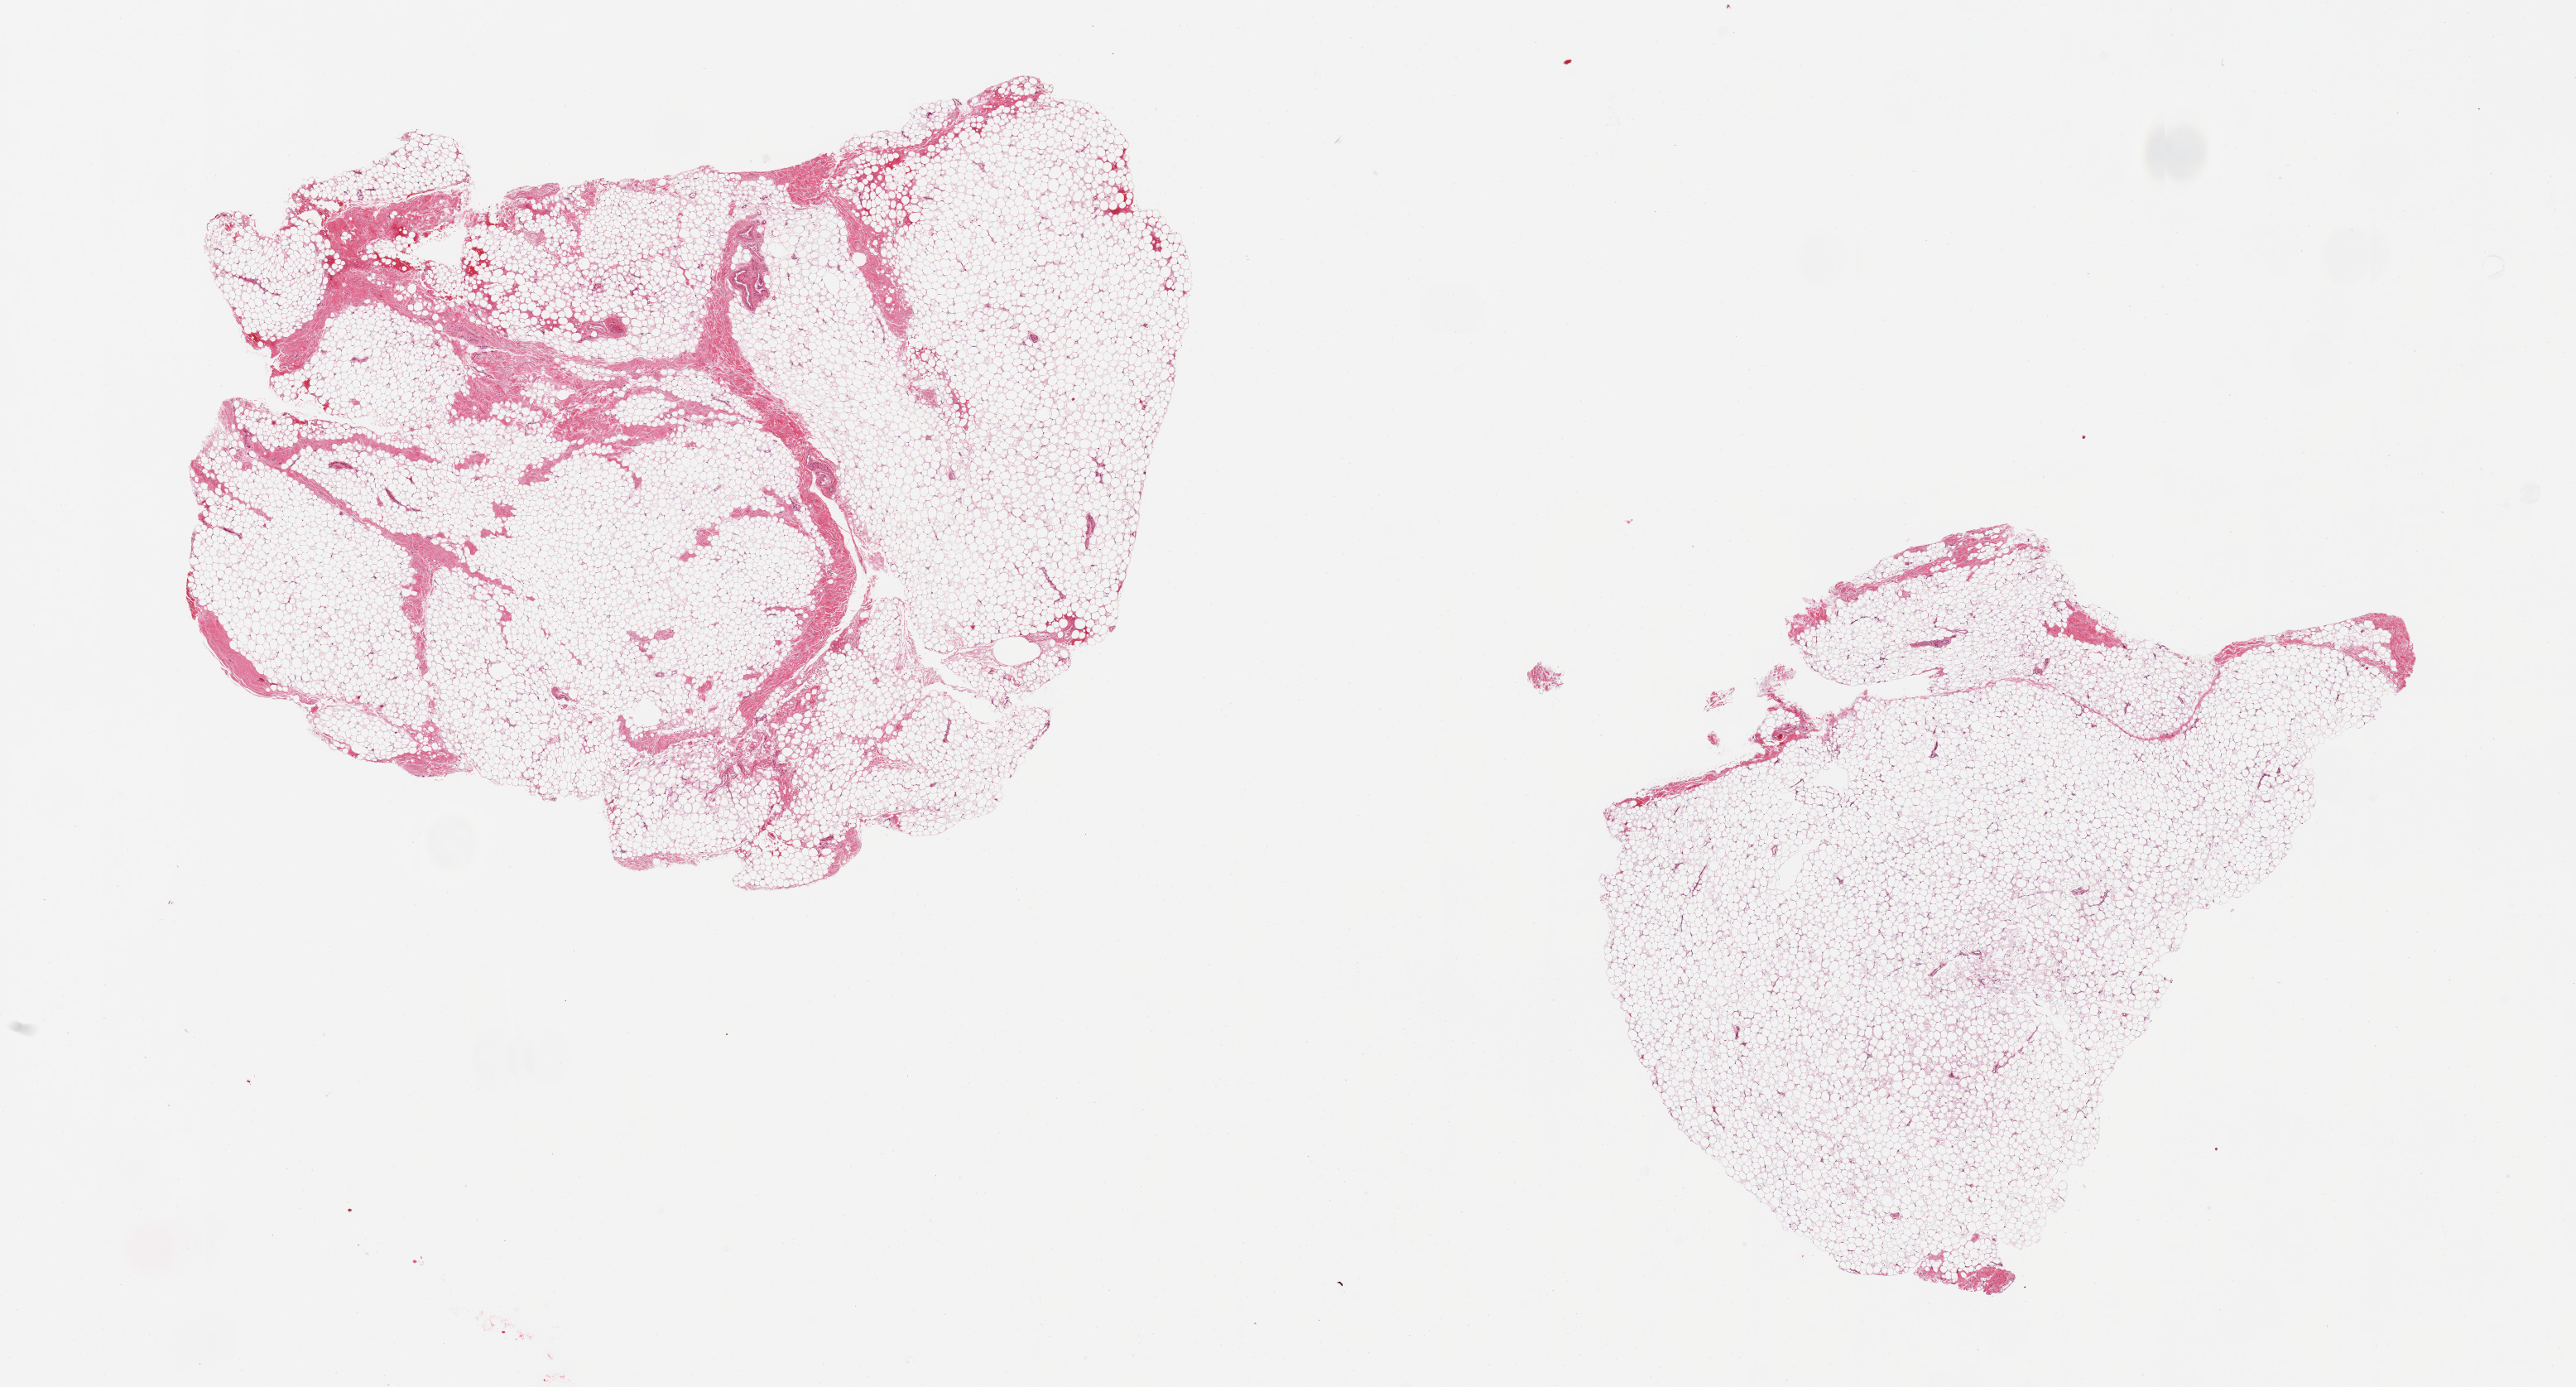
Whole-slide image, hematoxylin and eosin (H&E) stain, whole scanned area (about 24.6 x 13.2 mm, slide scanned at 20x) shown as a low-resolution overview, PAXgene-fixed, paraffin-embedded tissue, sampled site (target tissue): breast, tissue donor sample.
Reviewer comment on this tissue sample: 2 pieces; adipose tissue with fibrovascular component and no evidence of ductal structures.